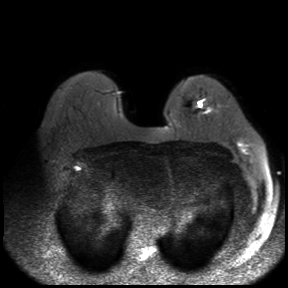
Breast MRI, one axial slice; diffusion-weighted series; image 2 of 4 stored at this slice position (different b-values; order by instance number); 3 T; 288 × 288 image matrix, field of view 360 × 360 mm. Female patient.
Annotated regions visible in this slice (outlined manually by an expert reader):
- tumour on diffusion-weighted imaging: bounding box [x1, y1, x2, y2] px = [198, 101, 203, 108]